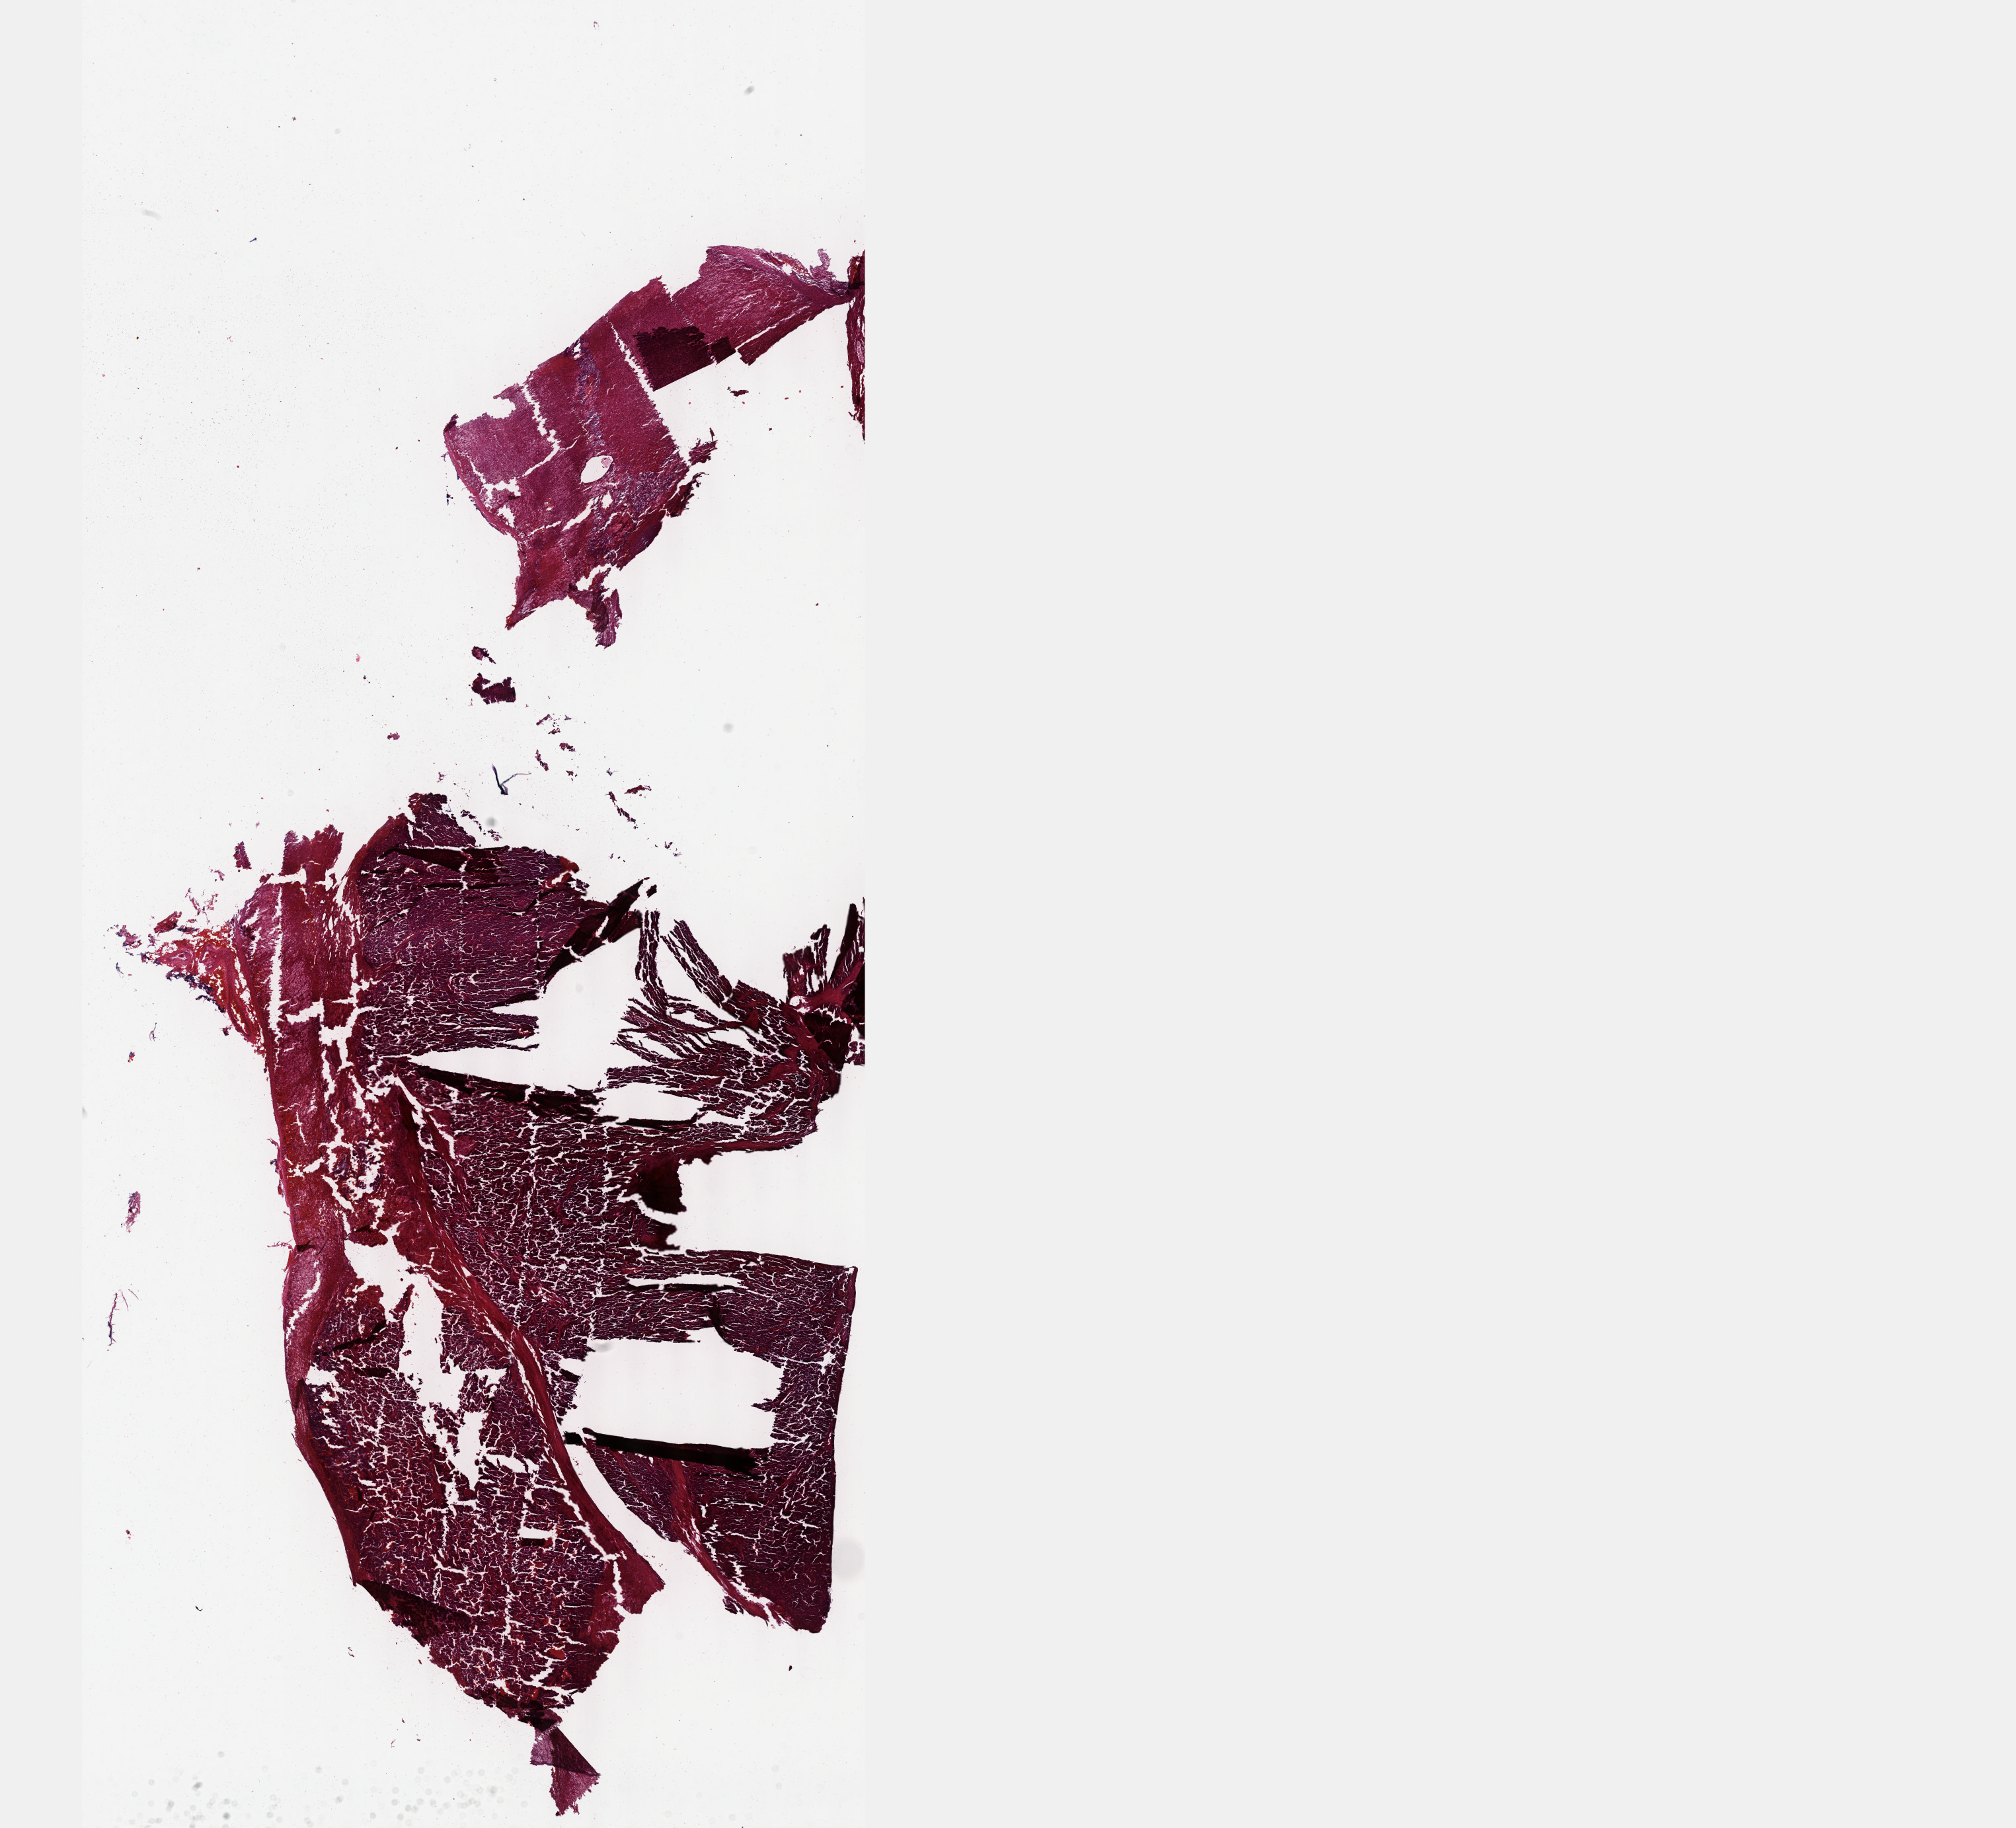
H&E-stained whole-slide image, shown as a low-resolution overview of the whole scanned area (about 24.6 x 22.4 mm, slide scanned at 40x); FFPE section; adrenal gland, primary tumour sample. Male patient; age at initial diagnosis 40 years.
Laterality: right. Histologic diagnosis: Pheochromocytoma, NOS.